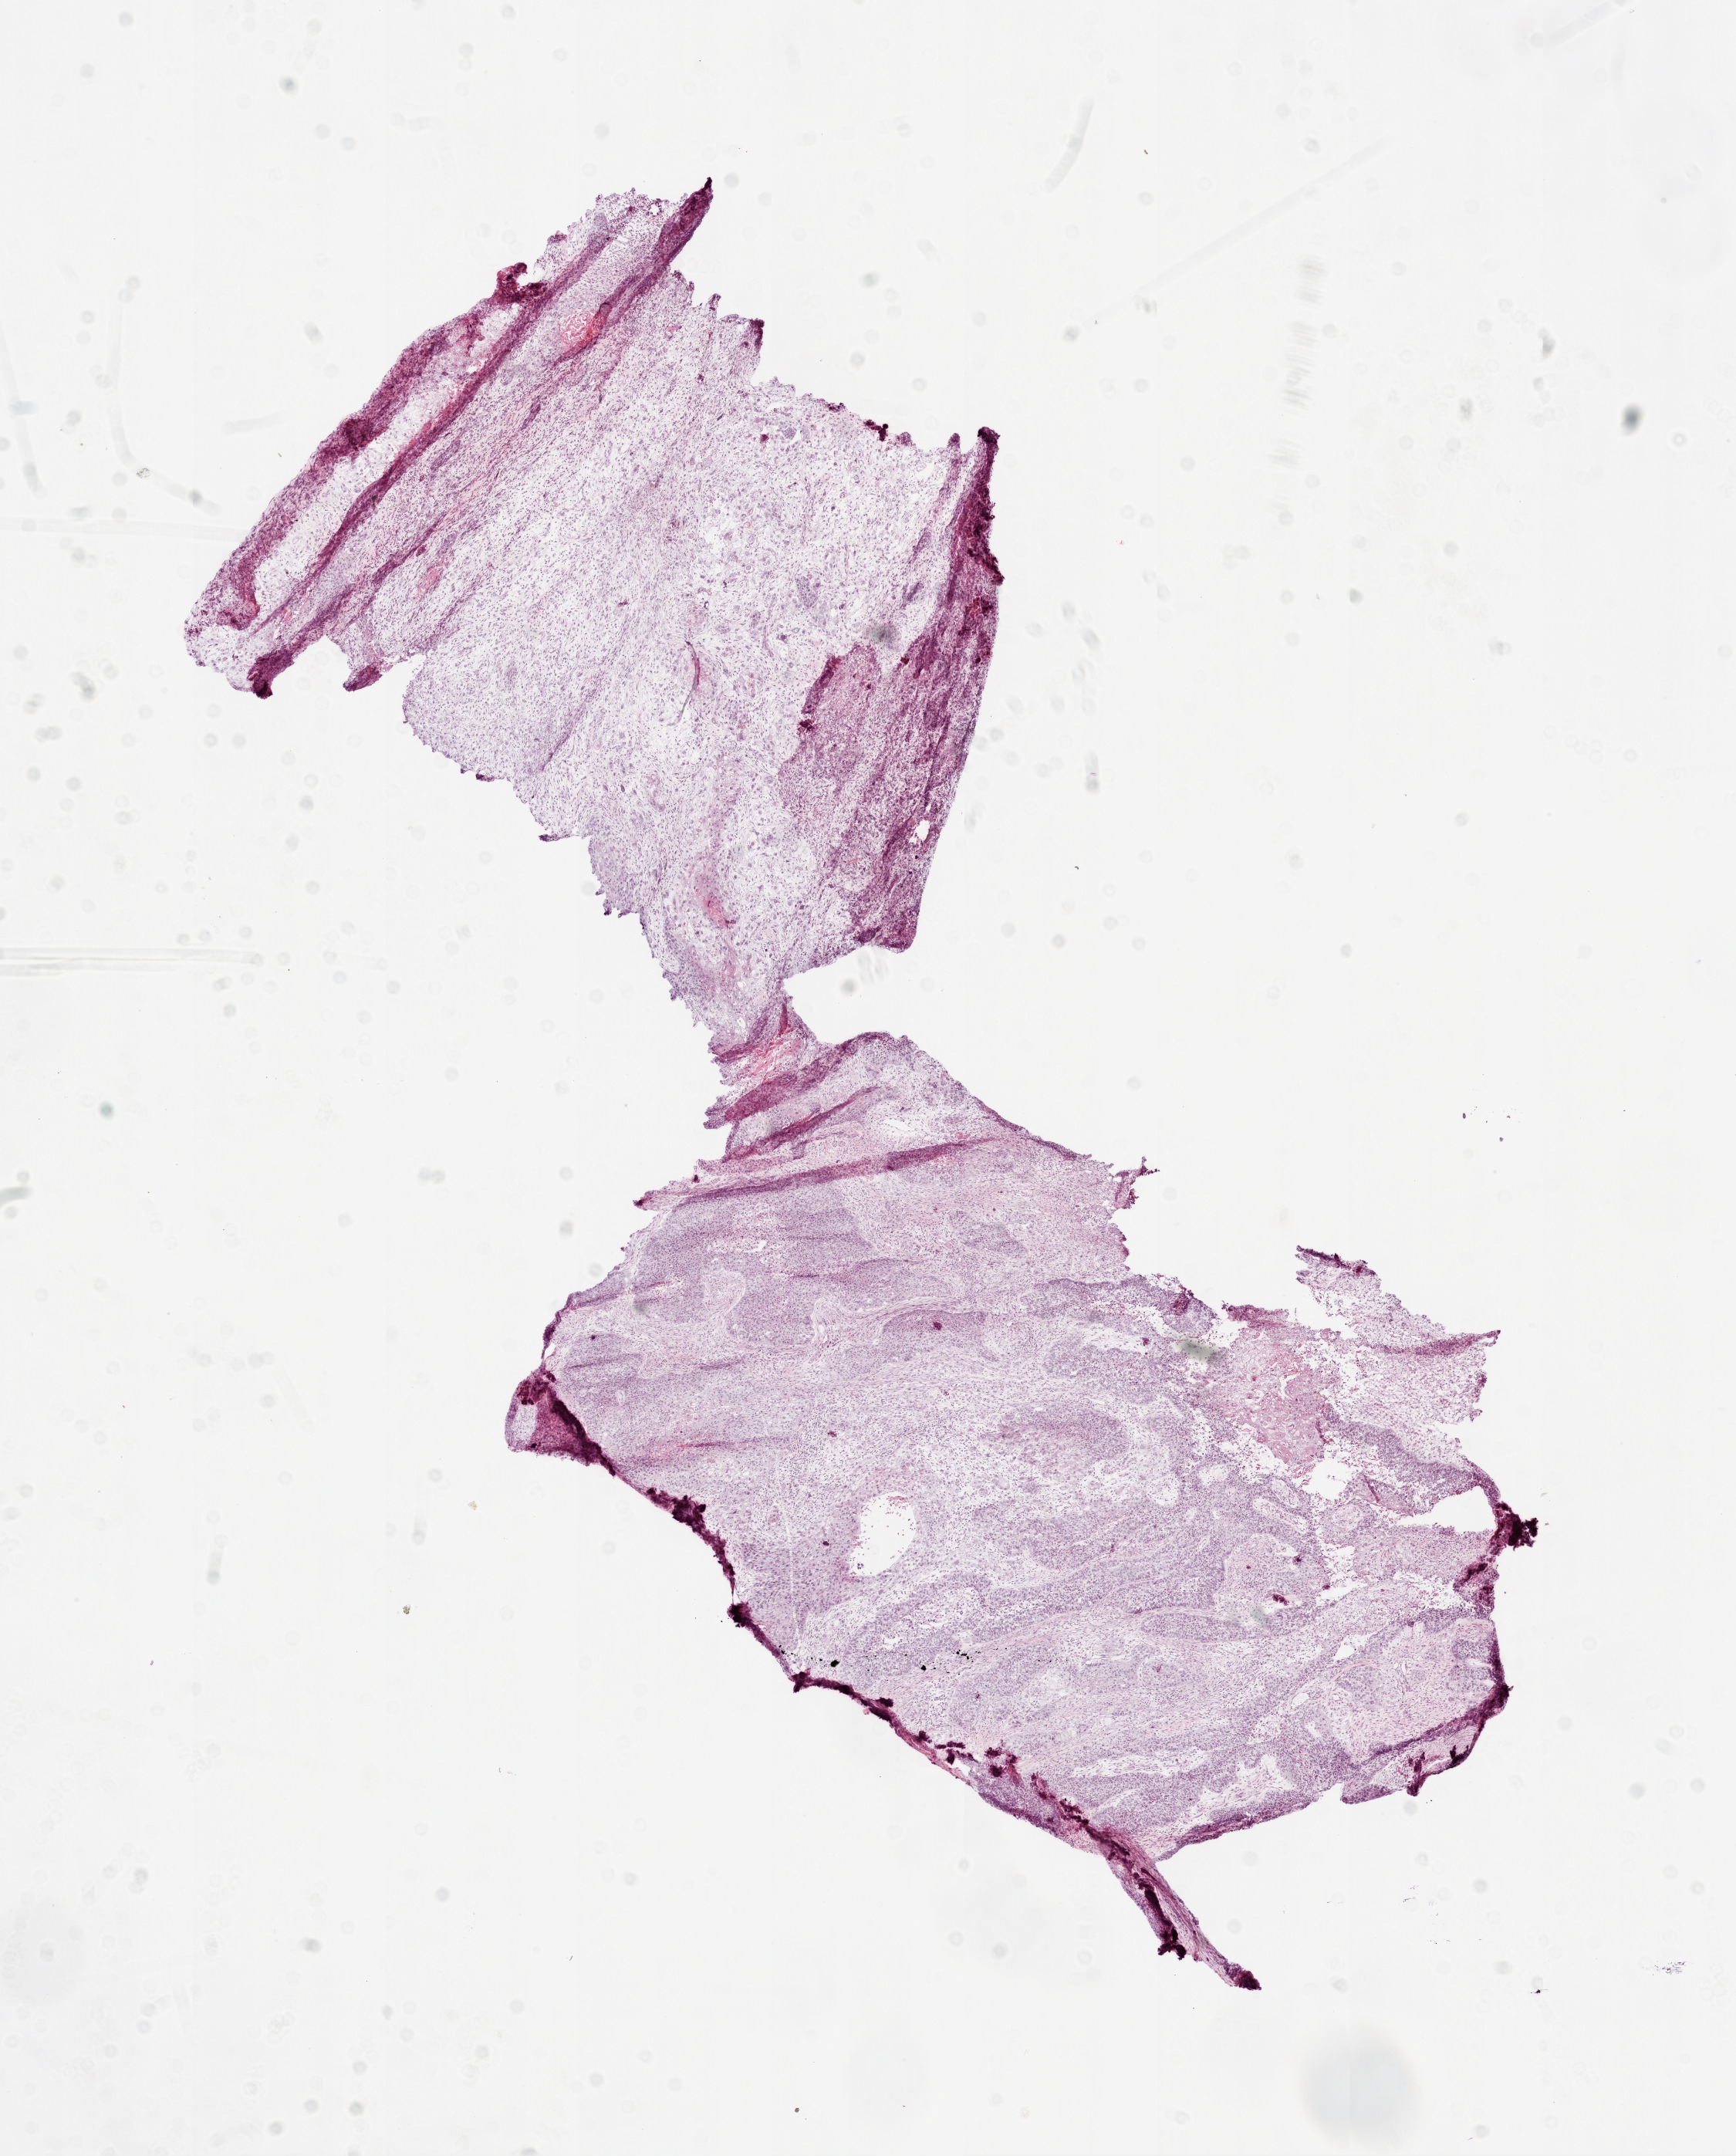
Digitized H&E-stained tissue section (whole slide), a low-resolution overview of the entire scanned area, about 9.0 x 11.2 mm. Frozen section from the top of the tissue portion. Lung, primary tumour sample. Female patient; age at initial diagnosis 64 years. Composition of this section per pathologist review: tumour cells 70%, tumour nuclei 70%, normal cells 0%, stromal cells 20%, necrosis 10%.
* laterality: left
* histologic diagnosis: Squamous cell carcinoma, NOS (lower lobe, lung)
* AJCC pathologic stage: IIB